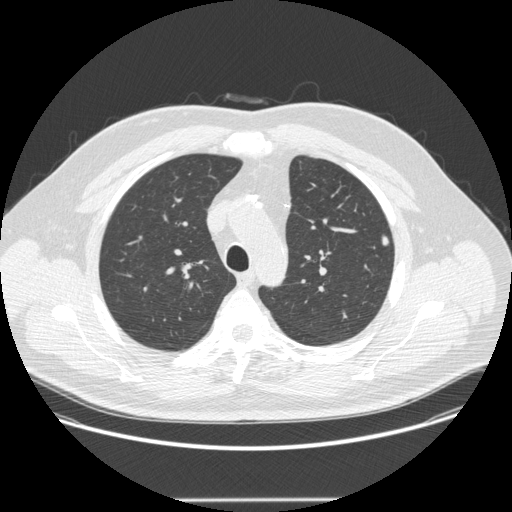
Chest CT (low-dose screening protocol), one axial image. Baseline annual screen. Lung window (W 1500 / L -600 HU). 1.25 mm slice thickness. 512 × 512 image matrix. Male, age 55 years at enrolment. Former smoker at enrolment.
Expert reader's lesion annotation, bounding box [x1, y1, x2, y2] px = [373, 231, 402, 259]. Screening reader's record for this exam (one nodule recorded; not confirmed to be the boxed lesion): non-calcified nodule or mass ≥4 mm, left upper lobe, 5 × 4 mm, smooth margins, soft tissue attenuation. Later outcome: lung cancer diagnosed 462 days after this screen (after the second annual screen) — adenocarcinoma, NOS, left upper lobe, moderately differentiated (G2), stage IA (AJCC 6th edition), 9 mm at pathology.